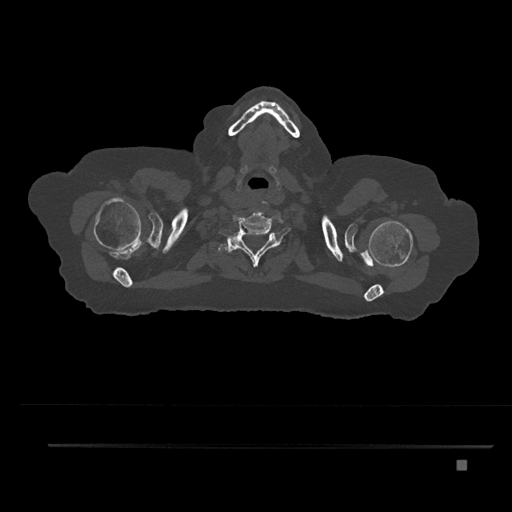
CT including the spine, one axial slice. Position 724 of 797 along the scan axis. 120 kVp. Bone window (W 1800 / L 400 HU). 512 × 512 image matrix, field of view 437 × 437 mm. Patient: female, 76 years. Case-level facts recorded for this patient, not image findings: primary cancer: lung; vertebrae with lytic lesions (as recorded): T11, L3.
Outlined on this slice (semi-automatically segmented with operator editing):
- T1 vertebra: bounding box [x1, y1, x2, y2] px = [225, 239, 261, 255]